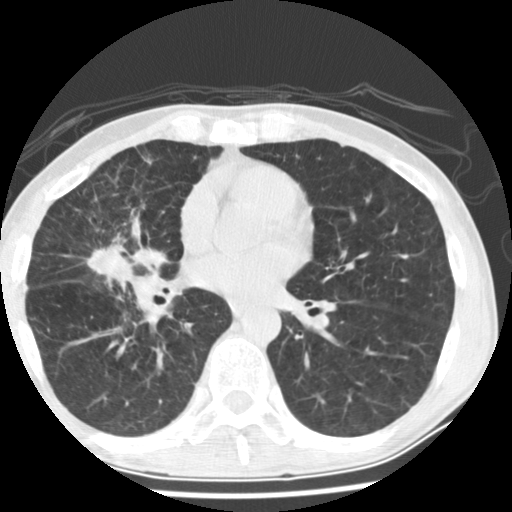
Low-dose screening chest CT, one axial slice; slice 78 of 162 in the series (ordered by position); reconstruction kernel STANDARD; lung window (W 1500 / L -600 HU); 2.5 mm slice thickness; 512 × 512 image matrix.
Outlined on this slice (expert manual segmentation):
- lesion 1 (tumor, middle lobe of right lung): bounding box [x1, y1, x2, y2] px = [72, 247, 119, 283]